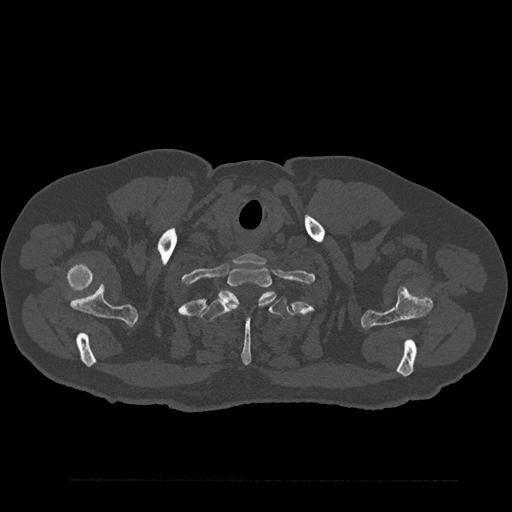
CT including the spine, one axial slice. Position 738 of 797 along the scan axis. Reconstruction kernel Br40s/3. Bone window (W 1800 / L 400 HU). 512 × 512 image matrix. Patient: male, 61 years. Case-level facts recorded for this patient, not image findings: primary cancer: prostate.
Annotated regions visible in this slice (semi-automatic segmentation, software-assisted and operator-edited):
- T1 vertebra: bounding box <218,267,272,310> (left, top, right, bottom; pixels)
- T2 vertebra: <201,291,295,366>